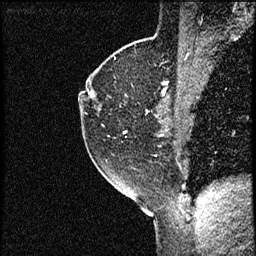
Breast MRI (dynamic contrast-enhanced), one sagittal slice; position 41 of 56 along the scan axis; dynamic contrast-enhanced study with each time point stored as its own series, time point 2 of 3 at this slice position (early post-contrast, ordered by acquisition time); 1.5 T; TE 4.2 ms, TR 17.3 ms; 2 mm slice thickness; 256 × 256 image matrix. Female patient. From the clinical record (not read from this slice): setting: breast cancer imaged before/during neoadjuvant chemotherapy; receptor status: HER2-positive.
Annotated regions visible in this slice (semi-automatic segmentation, software-assisted and operator-edited):
- analysis volume of interest (the breast-tissue region the enhancement analysis was run in; not a lesion): bounding box (x1, y1, x2, y2) in pixels: (78, 50, 156, 155)
- tumour enhancement mask (voxels above the 100 % enhancement threshold inside the analysis volume of interest): (88, 91, 148, 112)